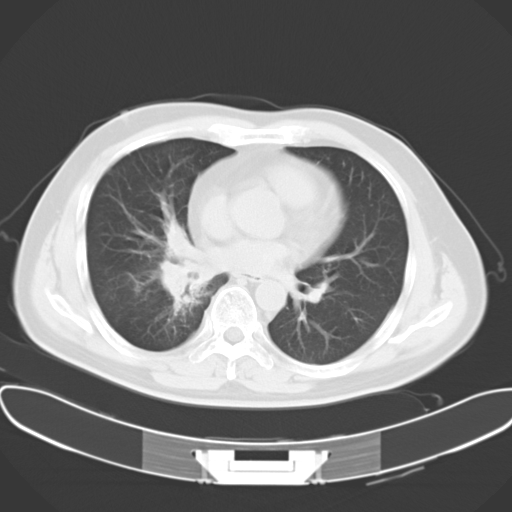
Chest CT, one axial slice; slice 14 of 28 in the series (ordered by position); lung window (W 1500 / L -600 HU); 10 mm slice thickness; 512 × 512 image matrix, field of view 388 × 388 mm. Patient: male, 48 years. Case-level facts recorded for this patient, not image findings: clinical TNM (as recorded): T1a N1 M1c.
Annotated regions visible in this slice (bounding box drawn by a radiologist):
- lung tumour (recorded histology: adenocarcinoma): bounding box [x1, y1, x2, y2] px = [161, 218, 219, 311]